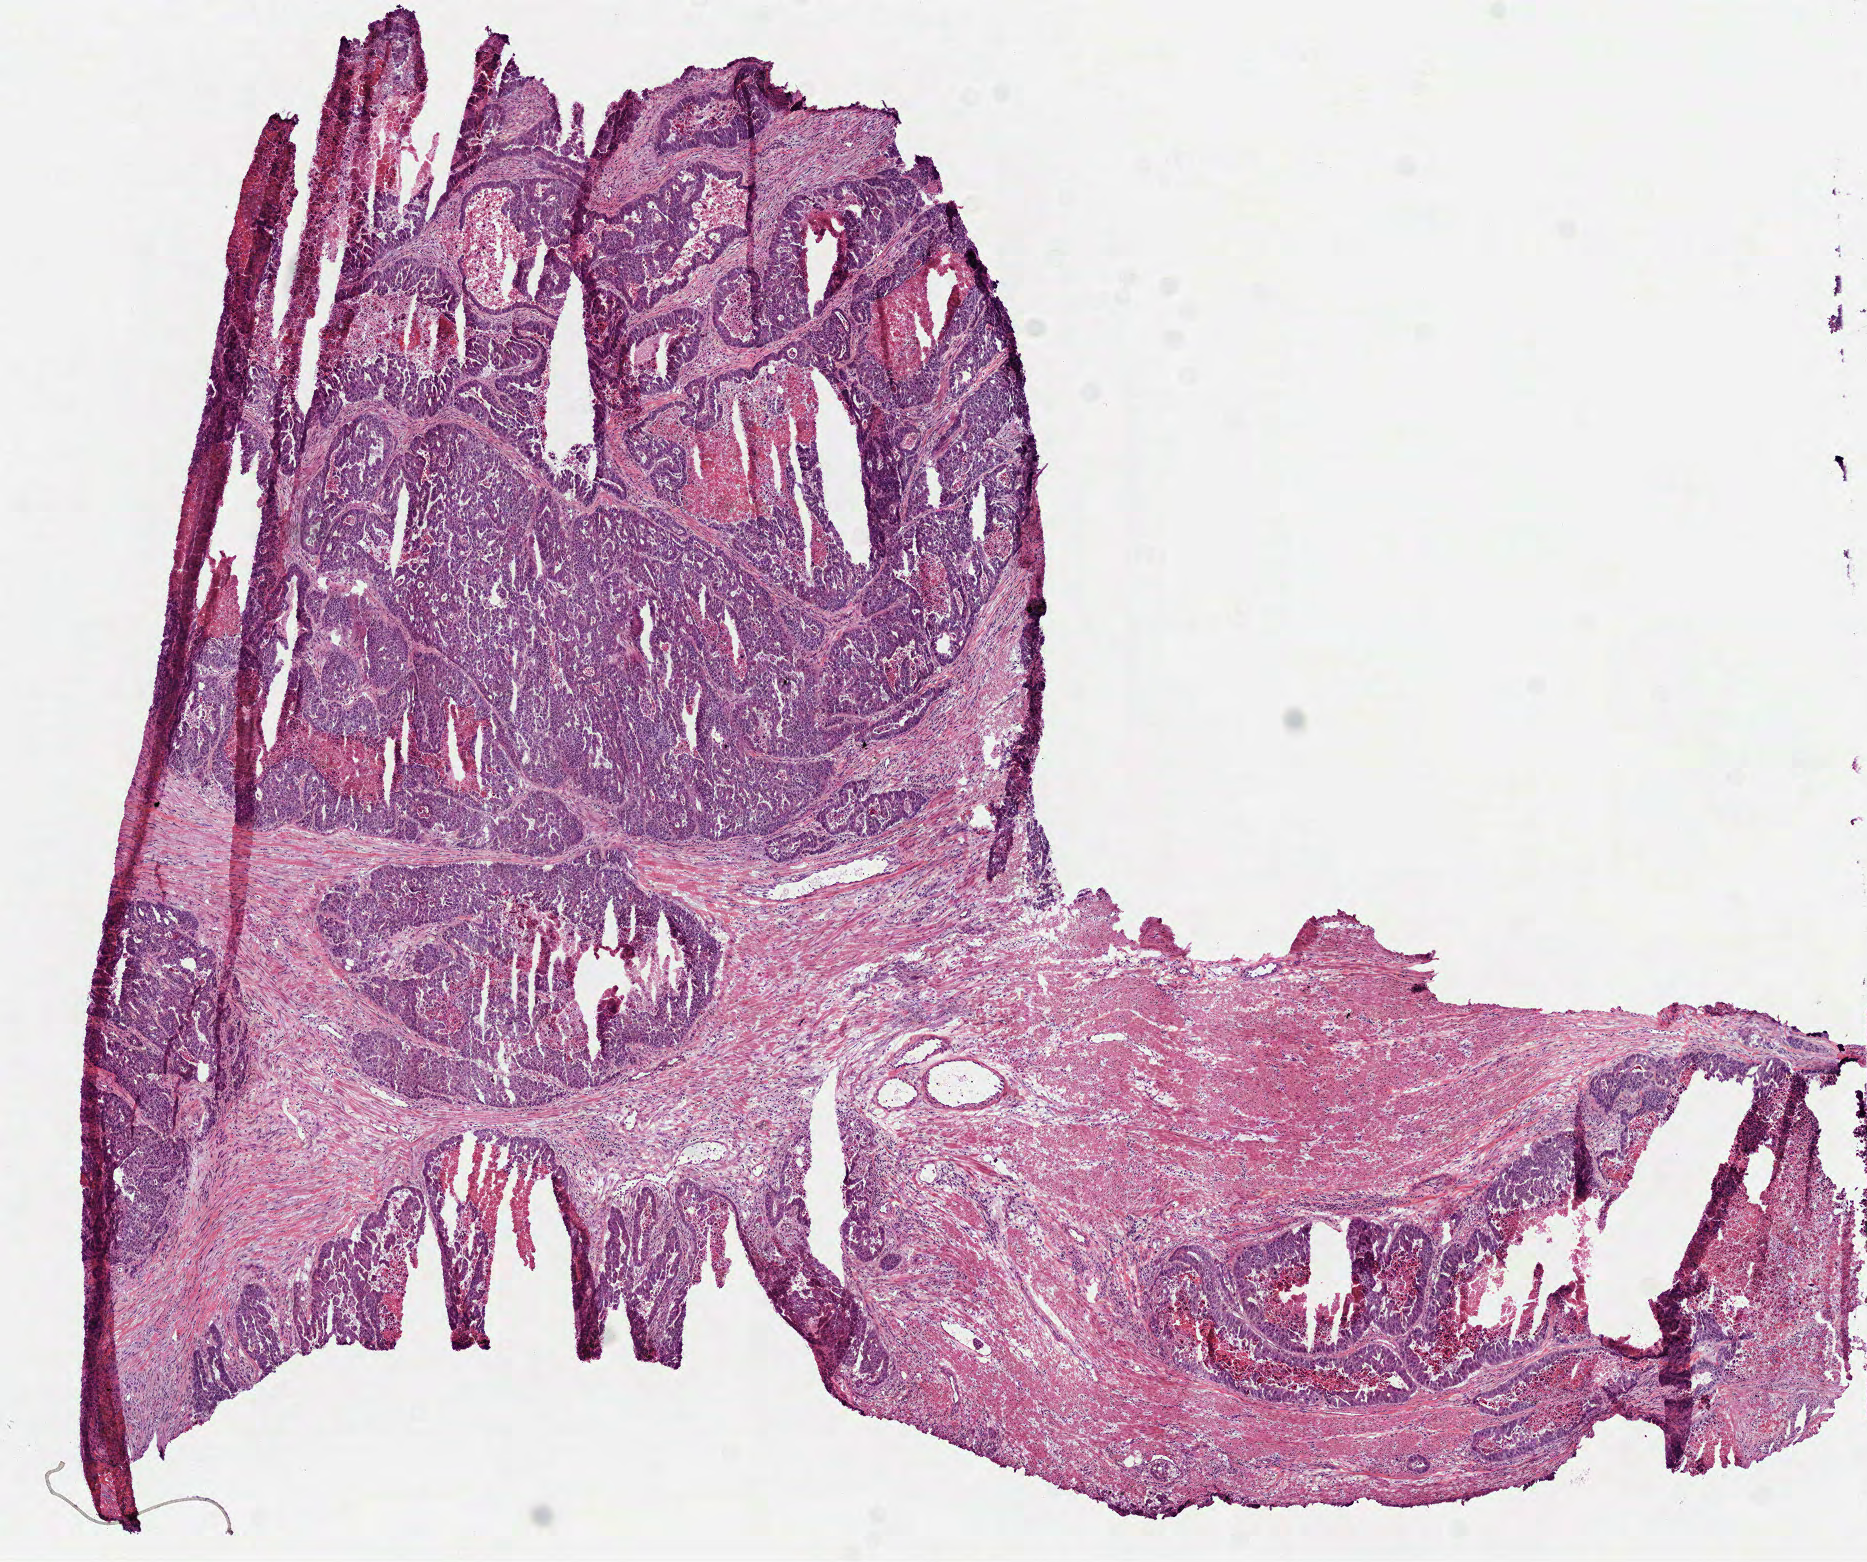
Digitized Hematoxylin and eosin (H&E) stained tissue section (whole slide), whole scanned area (about 7.5 x 6.3 mm) shown as a low-resolution overview, frozen section from the top of the tissue portion, sample: primary tumour, rectum. Patient: male, age at initial diagnosis 50 years. Pathologist review of this section (percent, as recorded): tumour cells 52%, tumour nuclei 85%, normal cells 0%, stromal cells 30%, necrosis 18%.
Lymph nodes positive (case pathology): 8 of 15 examined. AJCC pathologic stage: IIIC (7th edition). Histologic diagnosis: Adenocarcinoma, NOS (rectosigmoid junction).